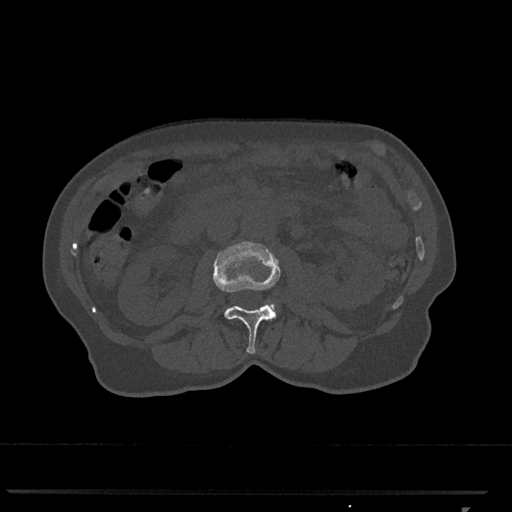
CT including the spine, one axial slice. Position 321 of 793 along the scan axis. Reconstruction kernel Br40s/3. 120 kVp. Bone window (W 1800 / L 400 HU). 512 × 512 image matrix, field of view 380 × 380 mm. Patient: female, 62 years. Case-level facts recorded for this patient, not image findings: primary cancer: renal.
Structures marked on this image (semi-automatically segmented with operator editing):
- L2 vertebra: bounding box <213,241,281,354> (left, top, right, bottom; pixels)
- L3 vertebra: <271,303,275,307>